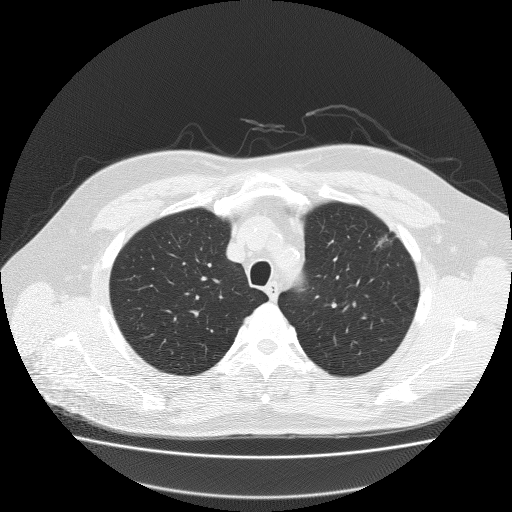
Low-dose screening chest CT, one axial slice; position 162 of 204 along the scan axis; reconstruction kernel FC51; 120 kVp; lung window (W 1500 / L -600 HU); 2 mm slice thickness; 512 × 512 image matrix, field of view 410 × 410 mm.
Structures marked on this image (expert manual segmentation):
- lesion 1 (tumor, upper lobe of left lung): bounding box [x1, y1, x2, y2] px = [376, 235, 390, 247]